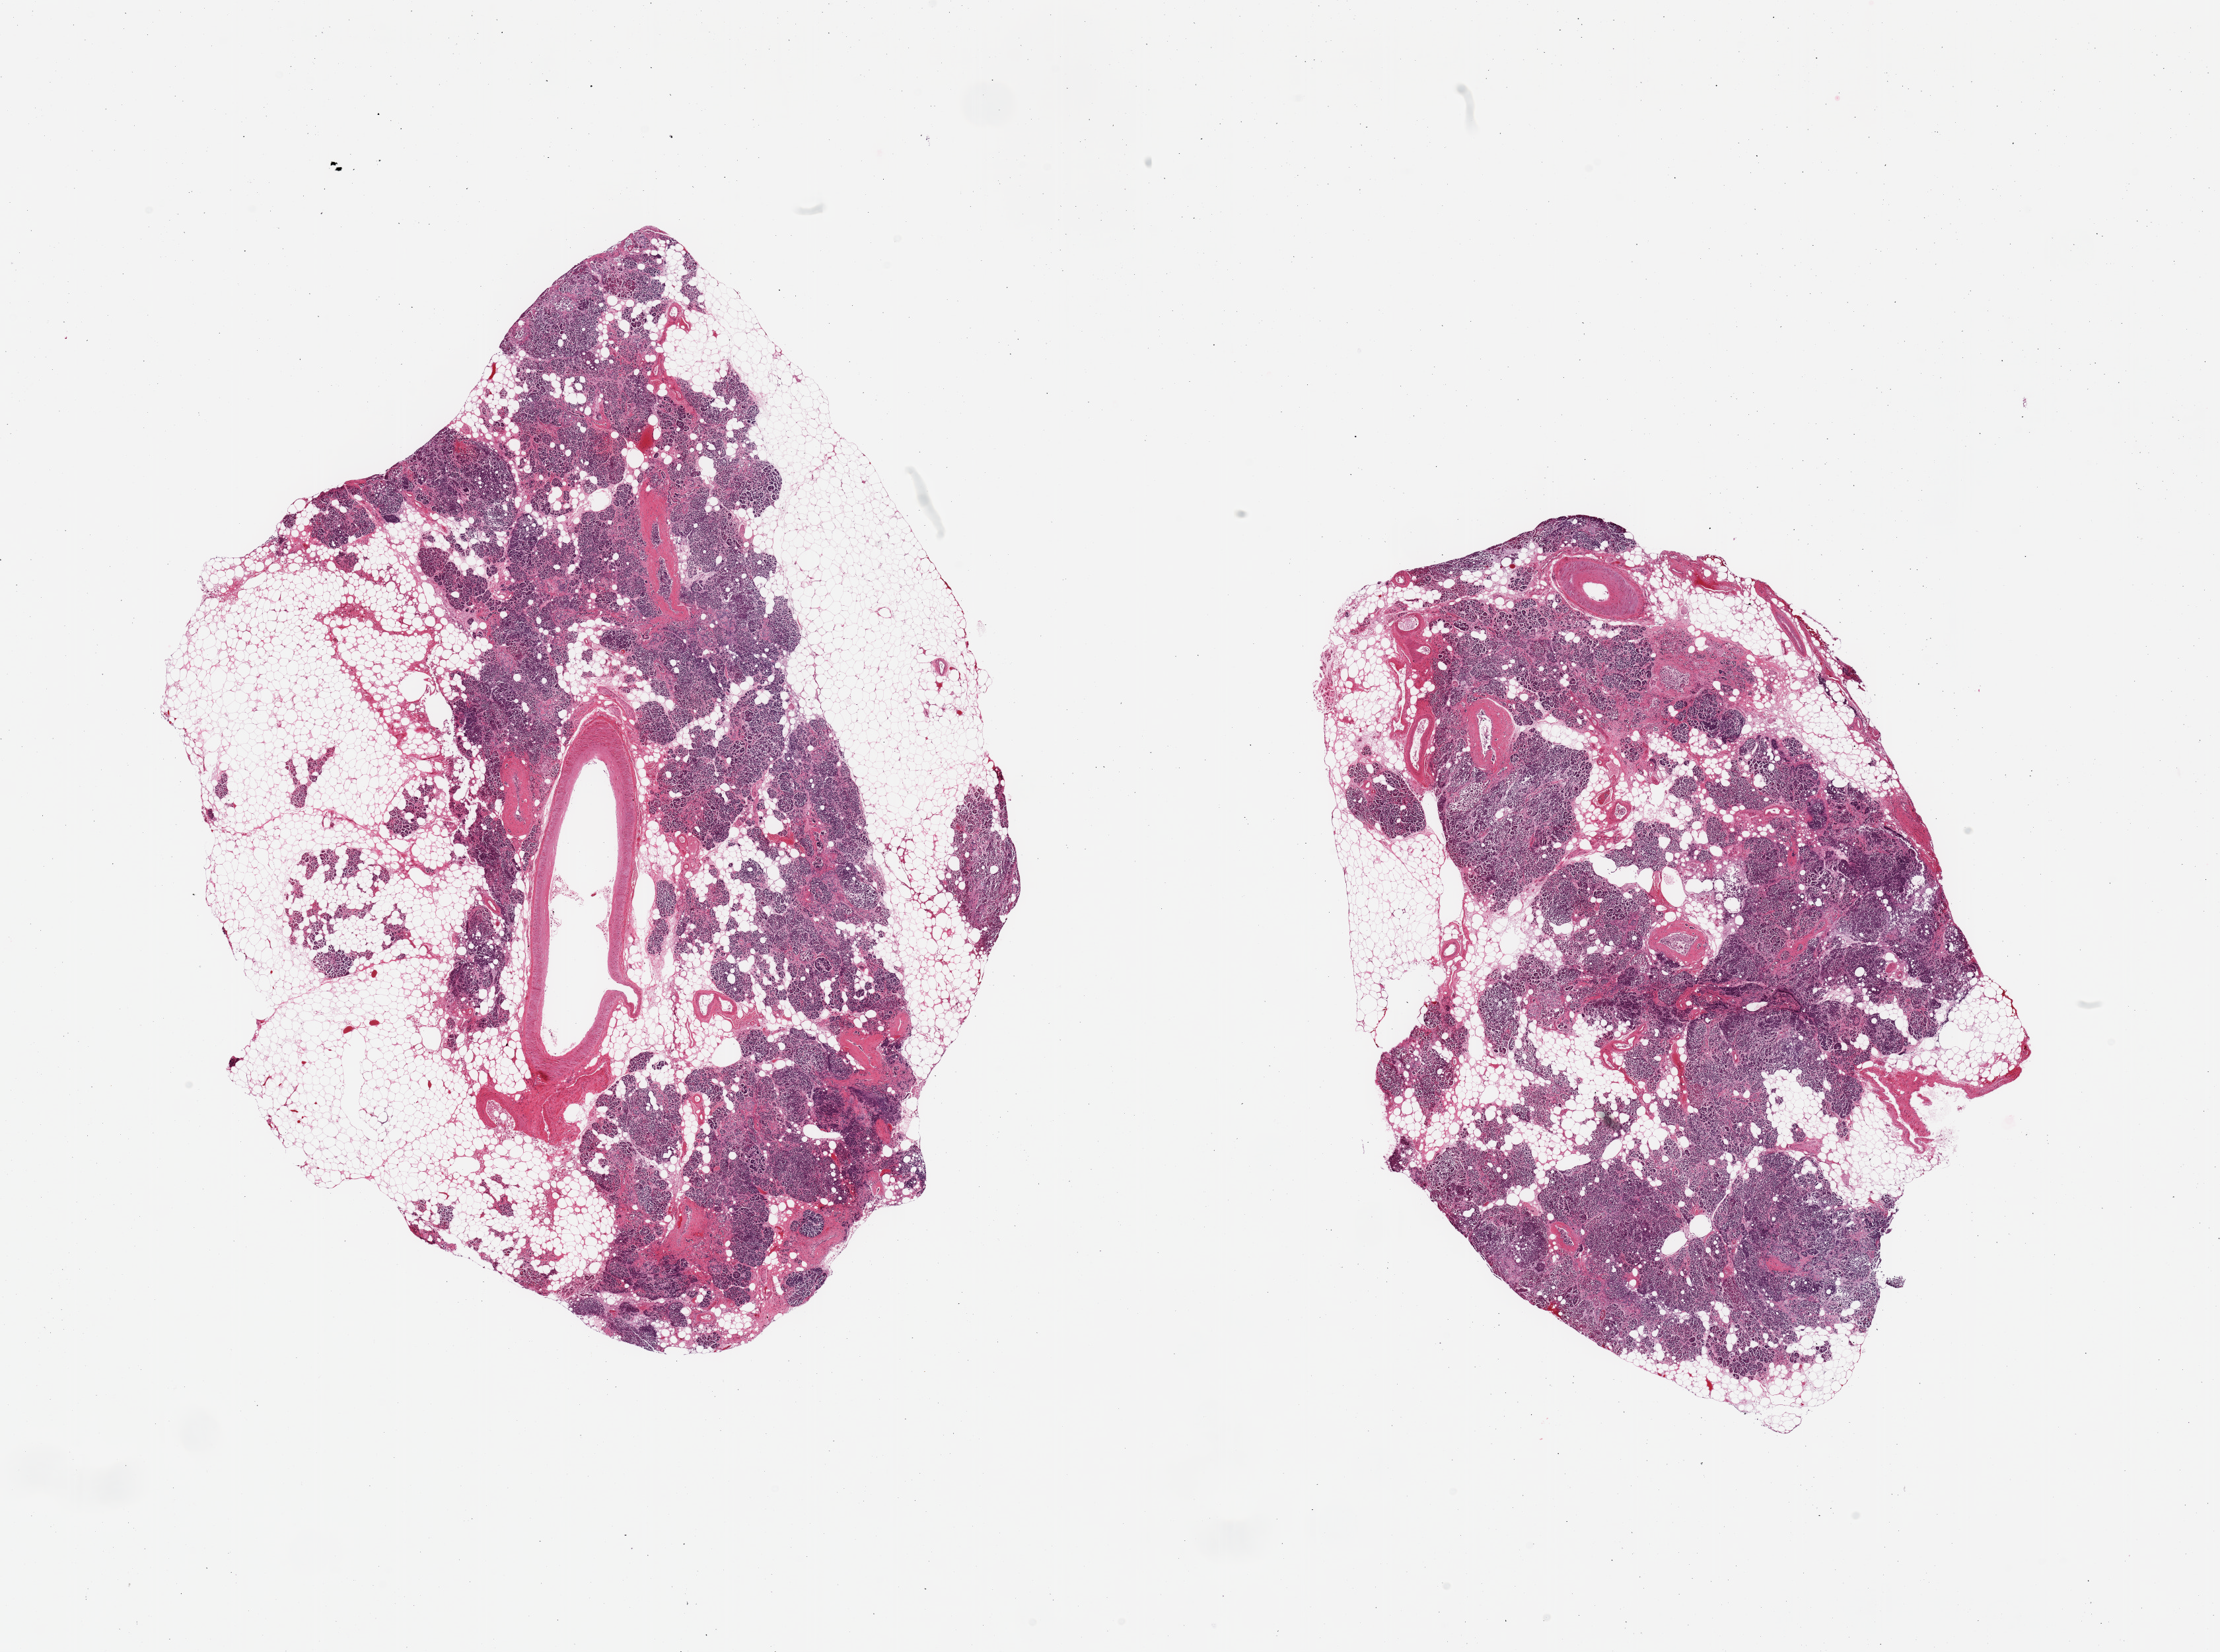
Hematoxylin and eosin (H&E) whole-slide image, a low-resolution overview of the entire scanned area, about 26.6 x 19.8 mm (acquisition: 20x scan). PAXgene-fixed, paraffin-embedded tissue. Target tissue: pancreas. Tissue donor sample. Female donor.
• reviewer comment on this tissue sample: 2 pieces; fat comprises 30 & 50%; some parts are severely autolyzed